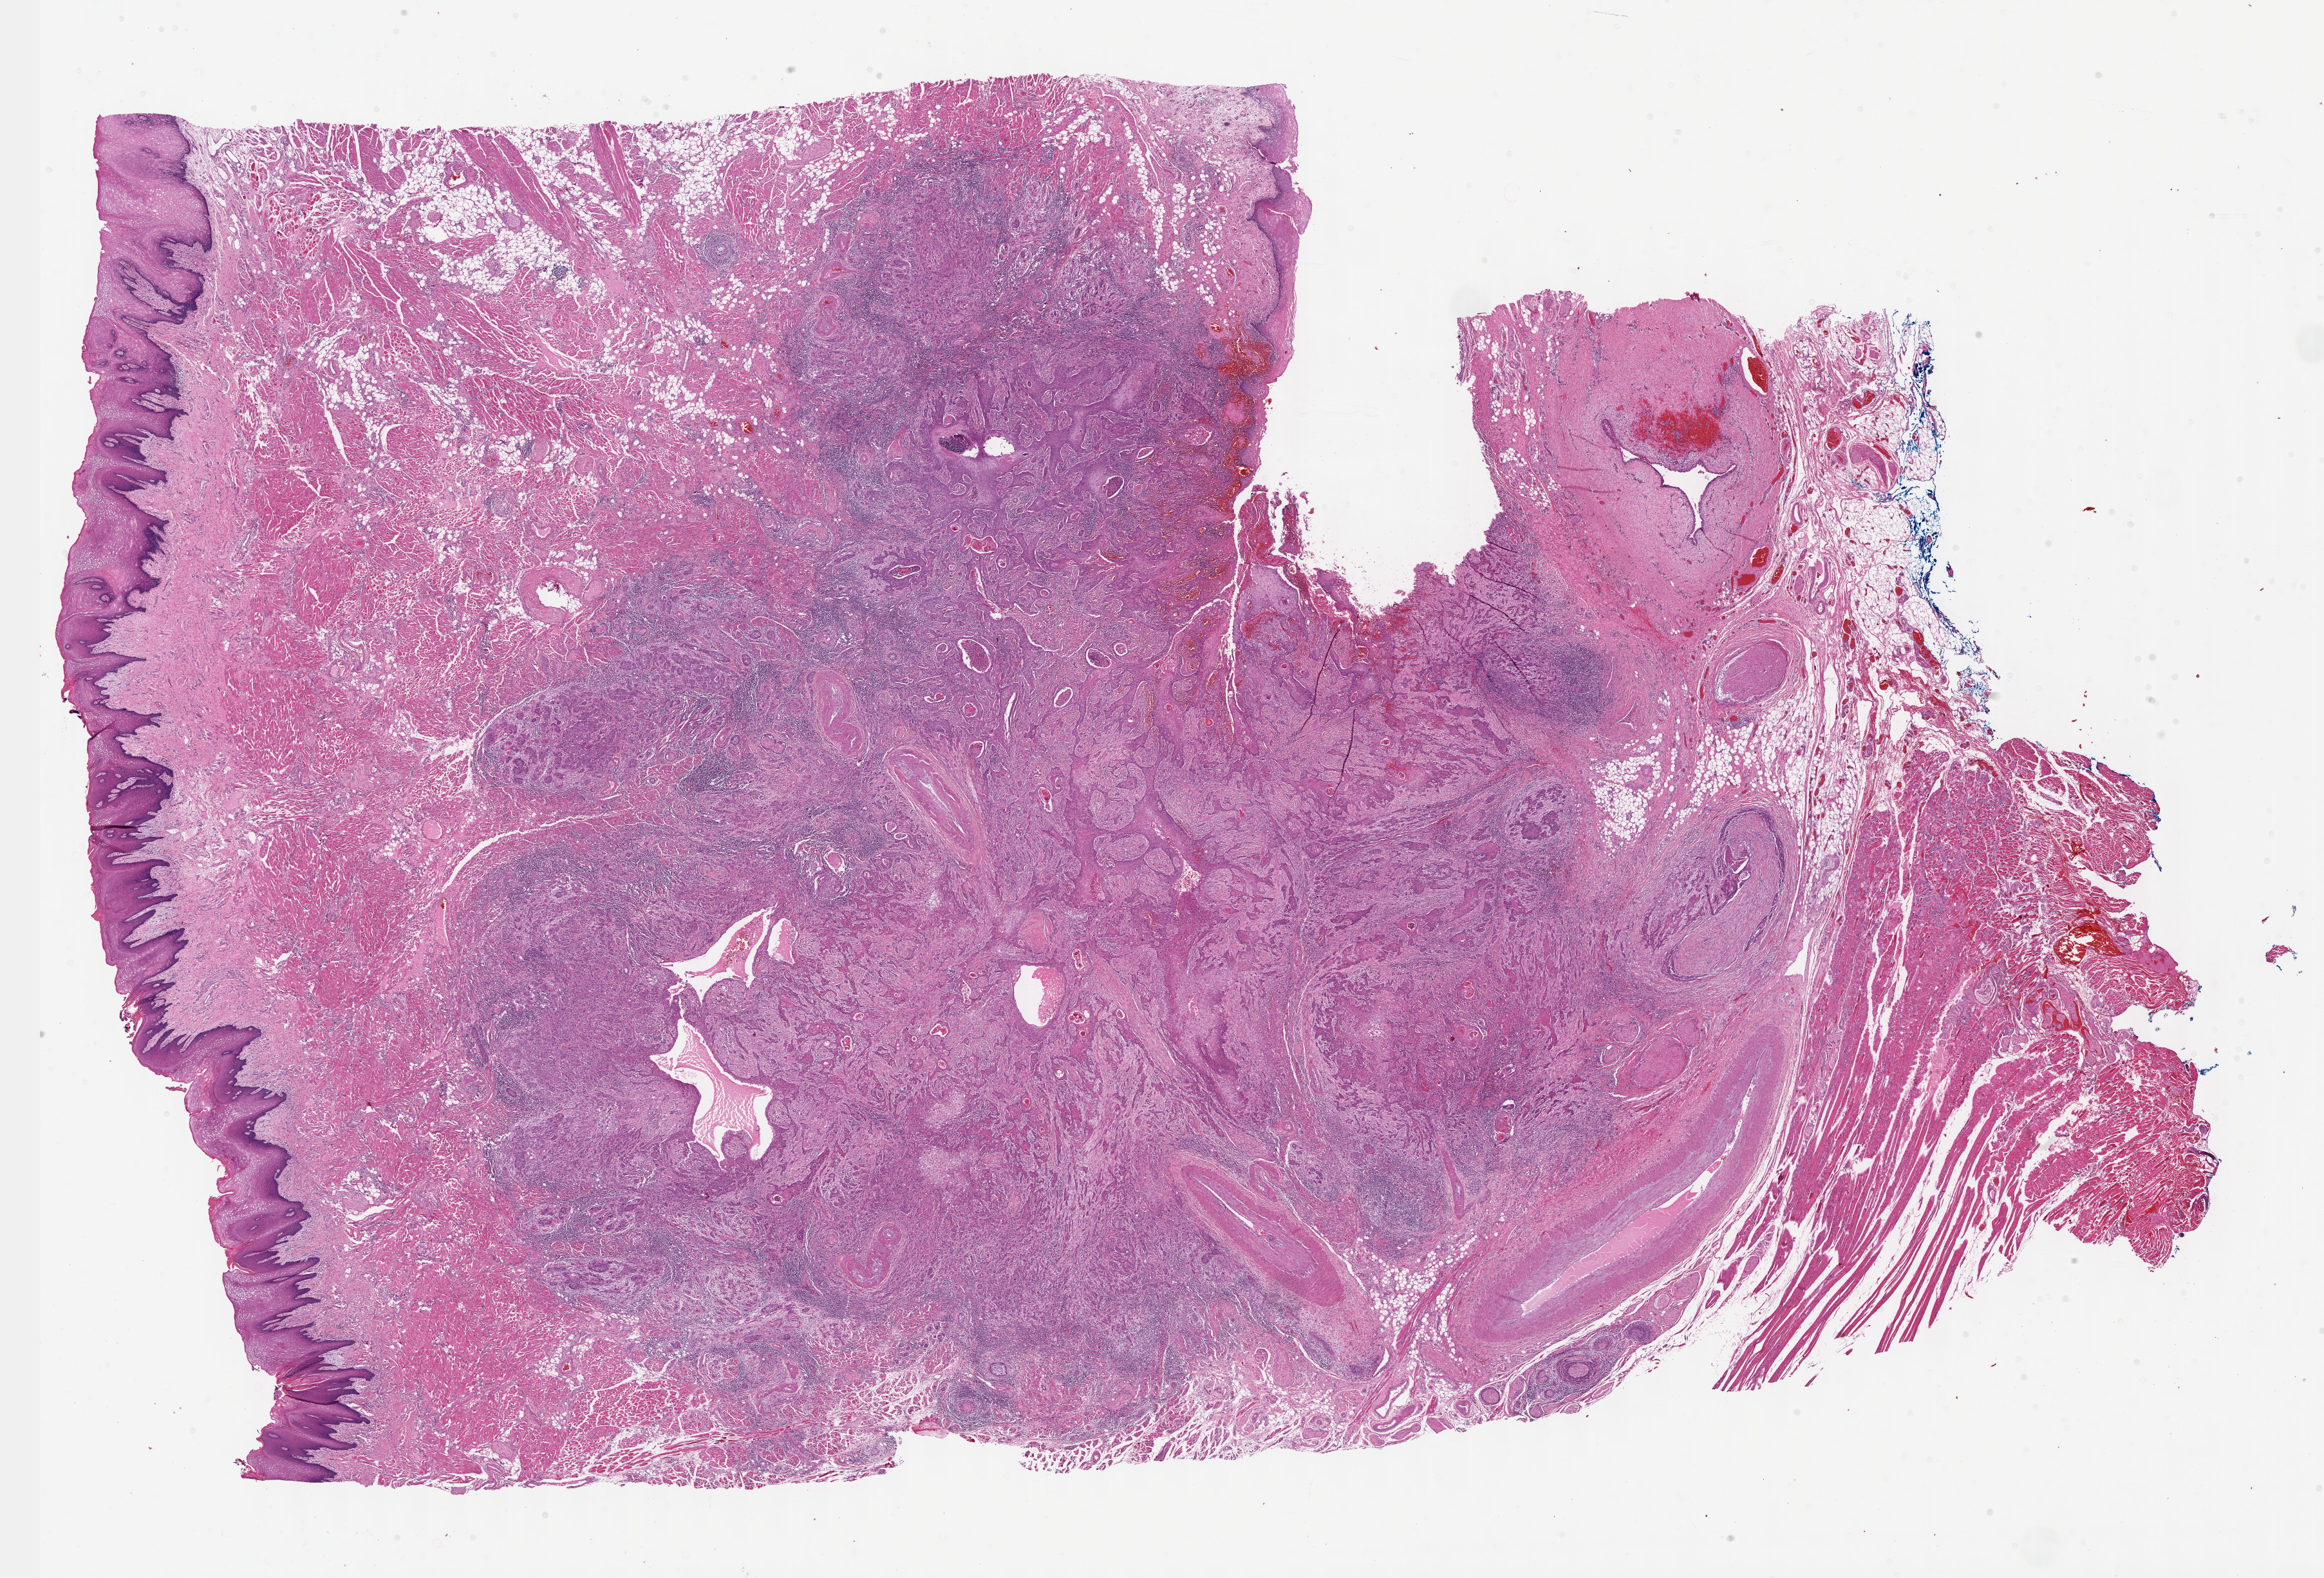
Digitized H&E-stained tissue section (whole slide), whole scanned area (about 29.2 x 19.8 mm, from a 40x scan) shown as a low-resolution overview. Formalin-fixed paraffin-embedded (FFPE) diagnostic section. Primary tumour sample from the head and neck. Patient: male, age at initial diagnosis 66 years.
Diagnosis: Squamous cell carcinoma, keratinizing, NOS (tongue, NOS).